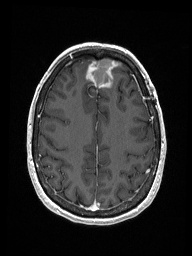
Brain MRI from a brain-tumour surgery series, one axial slice. Slice 53 of 192 in the series (ordered by position). T1-weighted post-contrast. 1 mm slice thickness. 192 × 256 image matrix. Case-level facts recorded for this patient, not image findings: histopathology: Metastastic Carcinoma from Breast primary; tumour location: Right Frontal.
Annotated regions visible in this slice (outlined manually by an expert reader):
- previous resection cavity: bounding box [x1, y1, x2, y2] px = [92, 59, 117, 85]